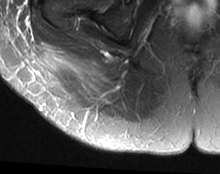
MRI of an extremity soft-tissue mass, one axial slice; position 13 of 63 along the scan axis; T2-weighted fat-saturated; MR volume resampled by the dataset authors to the PET/CT grid (not the native acquisition matrix); 3.27 mm slice thickness; 220 × 174 image matrix, field of view 215 × 170 mm. Female patient. Case-level facts recorded for this patient, not image findings: histological type: spindle cell suggestive of myxofibrosarcoma; grade: intermediate; site of the primary tumour: right buttock.
Outlined on this slice (expert contour drawn on MRI and transferred to this co-registered scan by the dataset authors):
- gross tumour volume (mass): box from (x=40, y=45) to (x=105, y=96) px